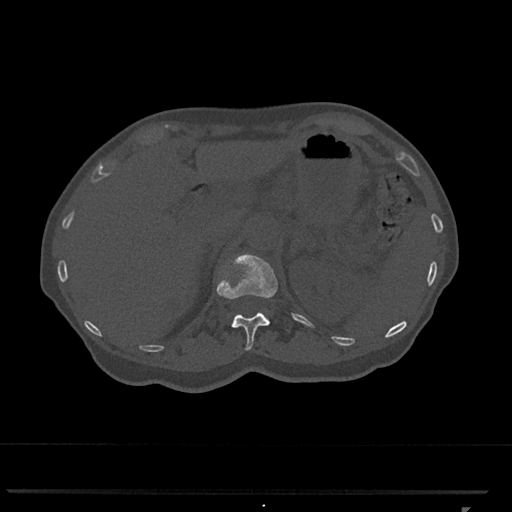
CT including the spine, one axial slice. Position 448 of 793 along the scan axis. 120 kVp. Bone window (W 1800 / L 400 HU). 0.5 mm slice thickness. 512 × 512 image matrix. Patient: female, 62 years. Case-level facts recorded for this patient, not image findings: primary cancer: renal.
Annotated regions visible in this slice (semi-automatic segmentation, software-assisted and operator-edited):
- T12 vertebra: bounding box (x1, y1, x2, y2) in pixels: (217, 254, 278, 350)